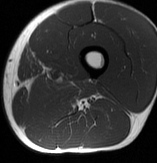
MRI of an extremity soft-tissue mass, one axial slice. Position 20 of 70 along the scan axis. MR volume resampled by the dataset authors to the PET/CT grid (not the native acquisition matrix). 3.27 mm slice thickness. 157 × 163 image matrix, field of view 153 × 159 mm. Male patient. Case-level facts recorded for this patient, not image findings: histological type: extraskeletal osteosarcoma; grade: high; site of the primary tumour: left adductur.
Outlined on this slice (expert contour drawn on MRI and transferred to this co-registered scan by the dataset authors):
- gross tumour volume (mass): bounding box <28,76,96,105> (left, top, right, bottom; pixels)